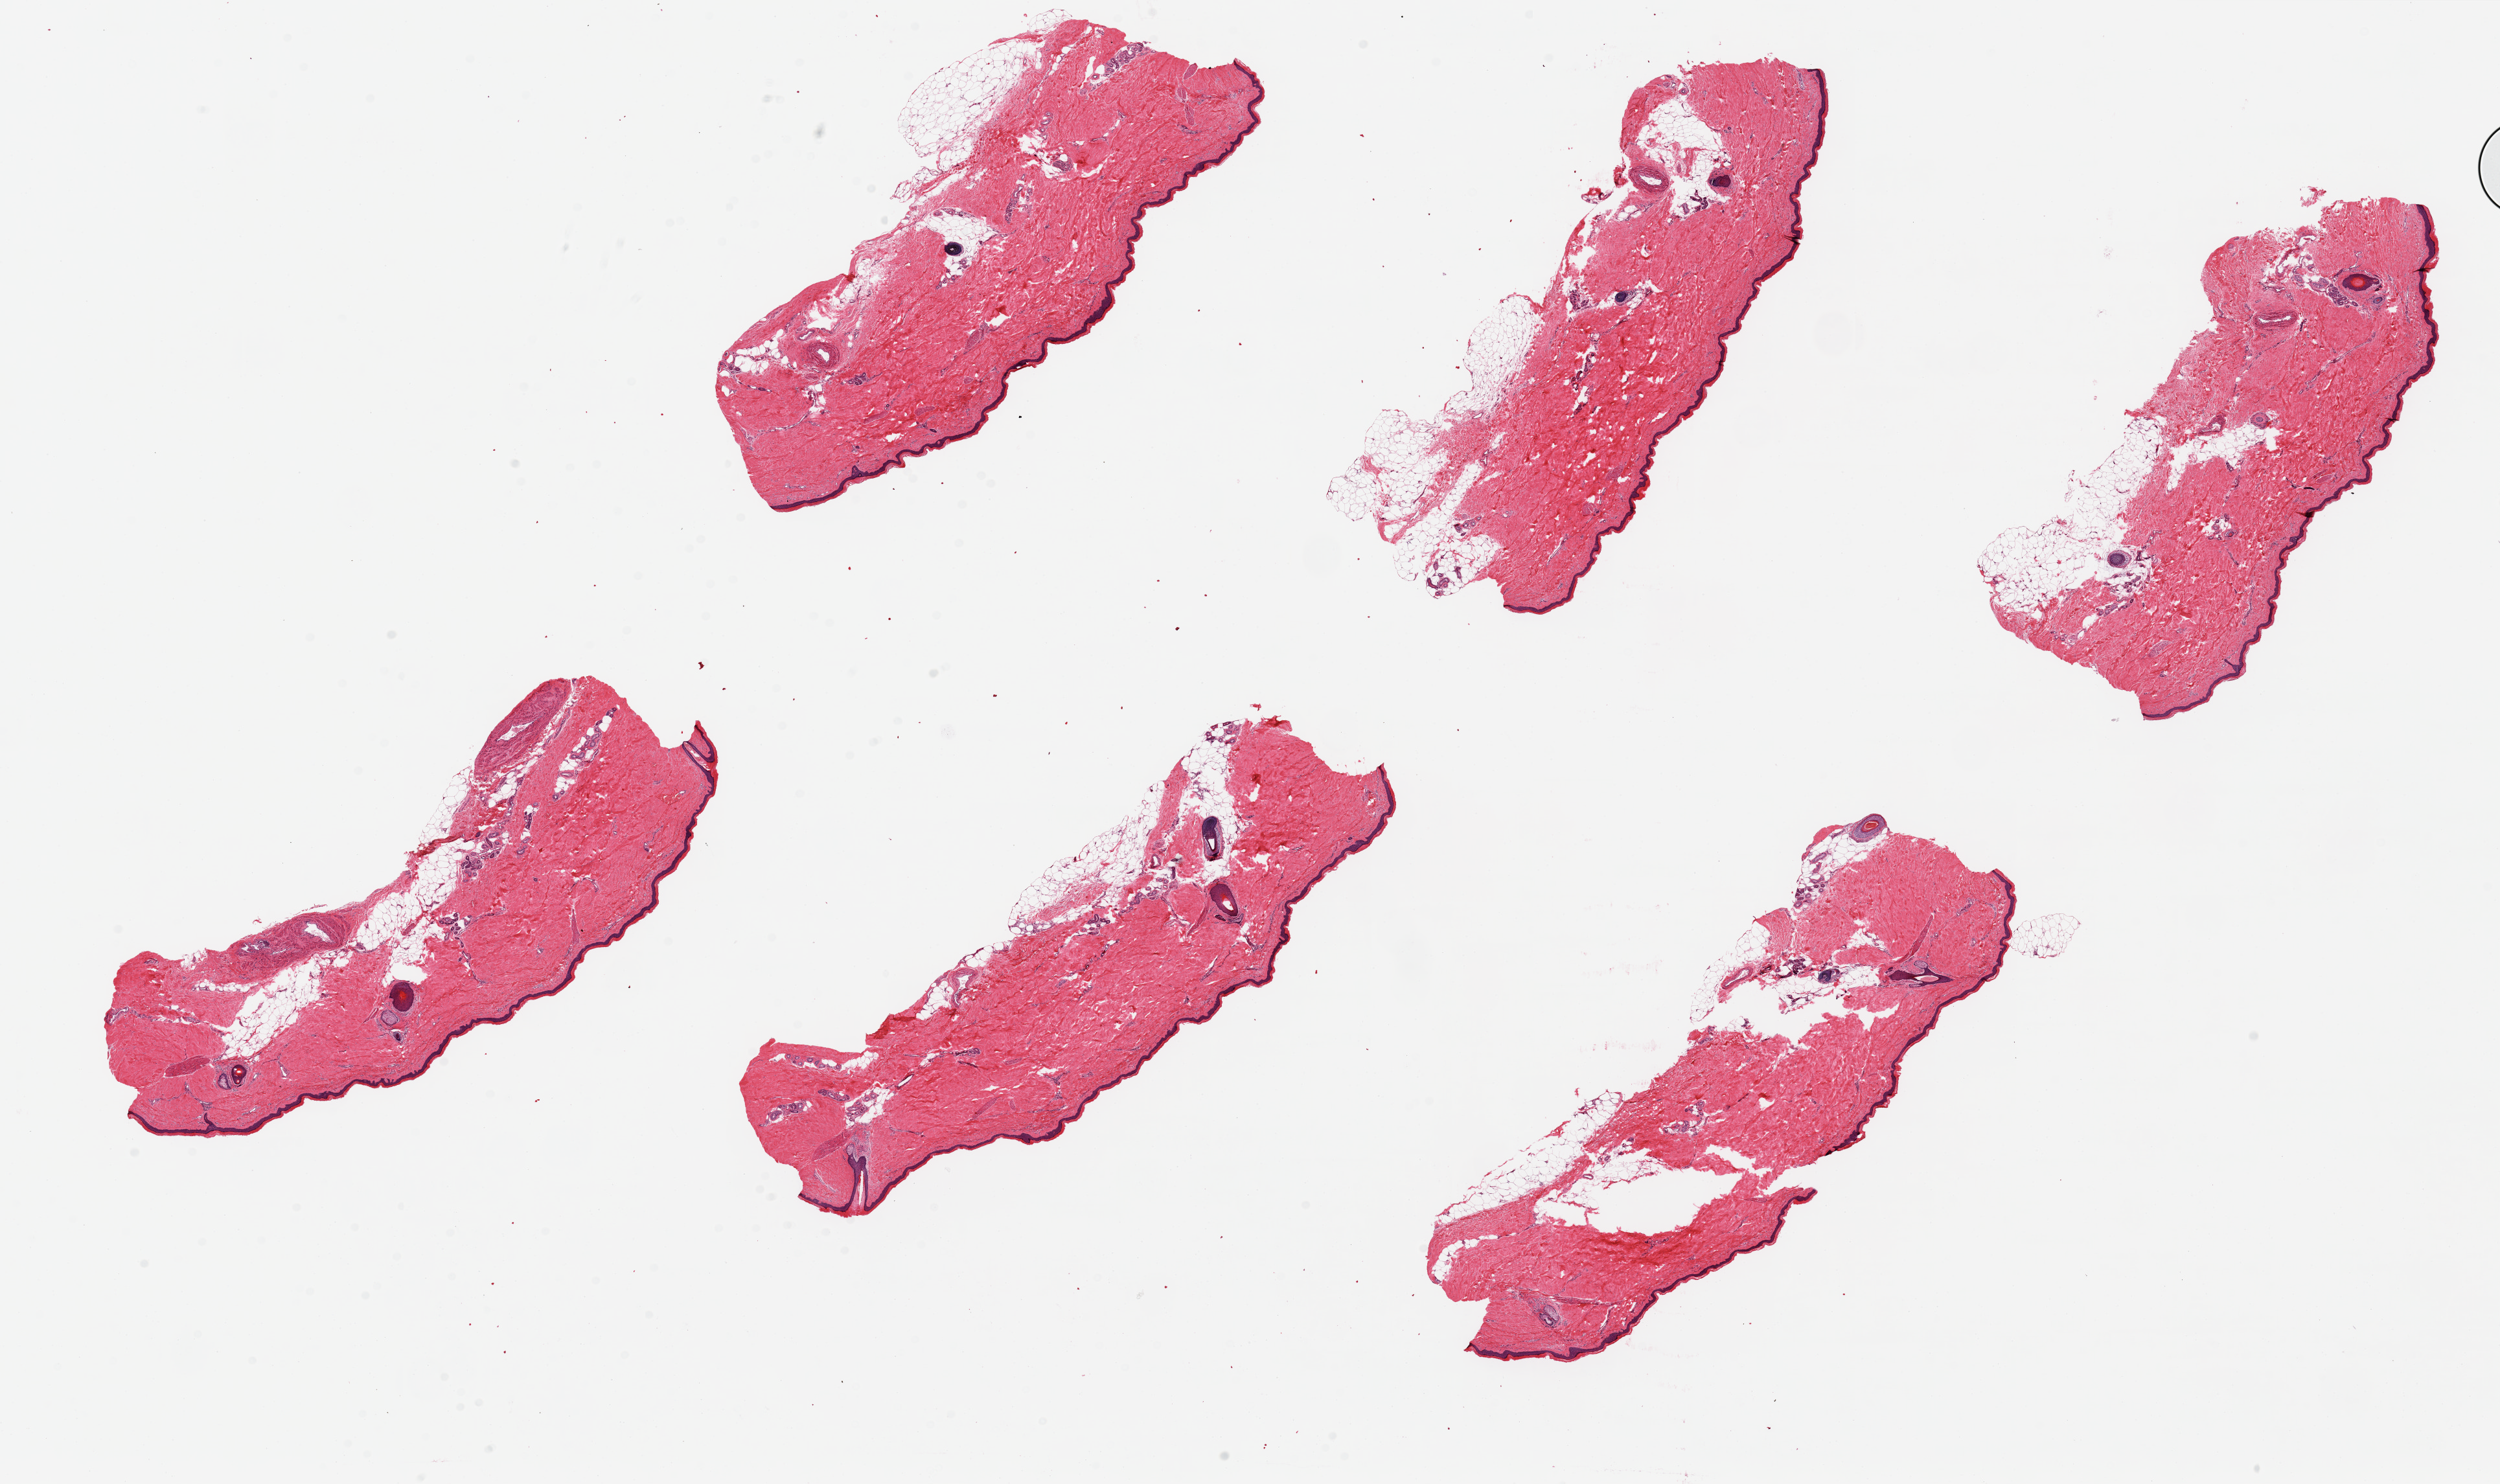
Whole-slide image, haematoxylin and eosin stain, shown as a low-resolution overview of the whole scanned area (about 30.5 x 18.1 mm, from a 20x scan); PAXgene-fixed paraffin-embedded (PFPE) section; sampled site (target tissue): skin of lower leg; tissue donor sample. Donor: male.
• reviewer comment on this tissue sample: 6 pieces ~8x3mm; squamous epithelium is ~1.5-2% of thickness